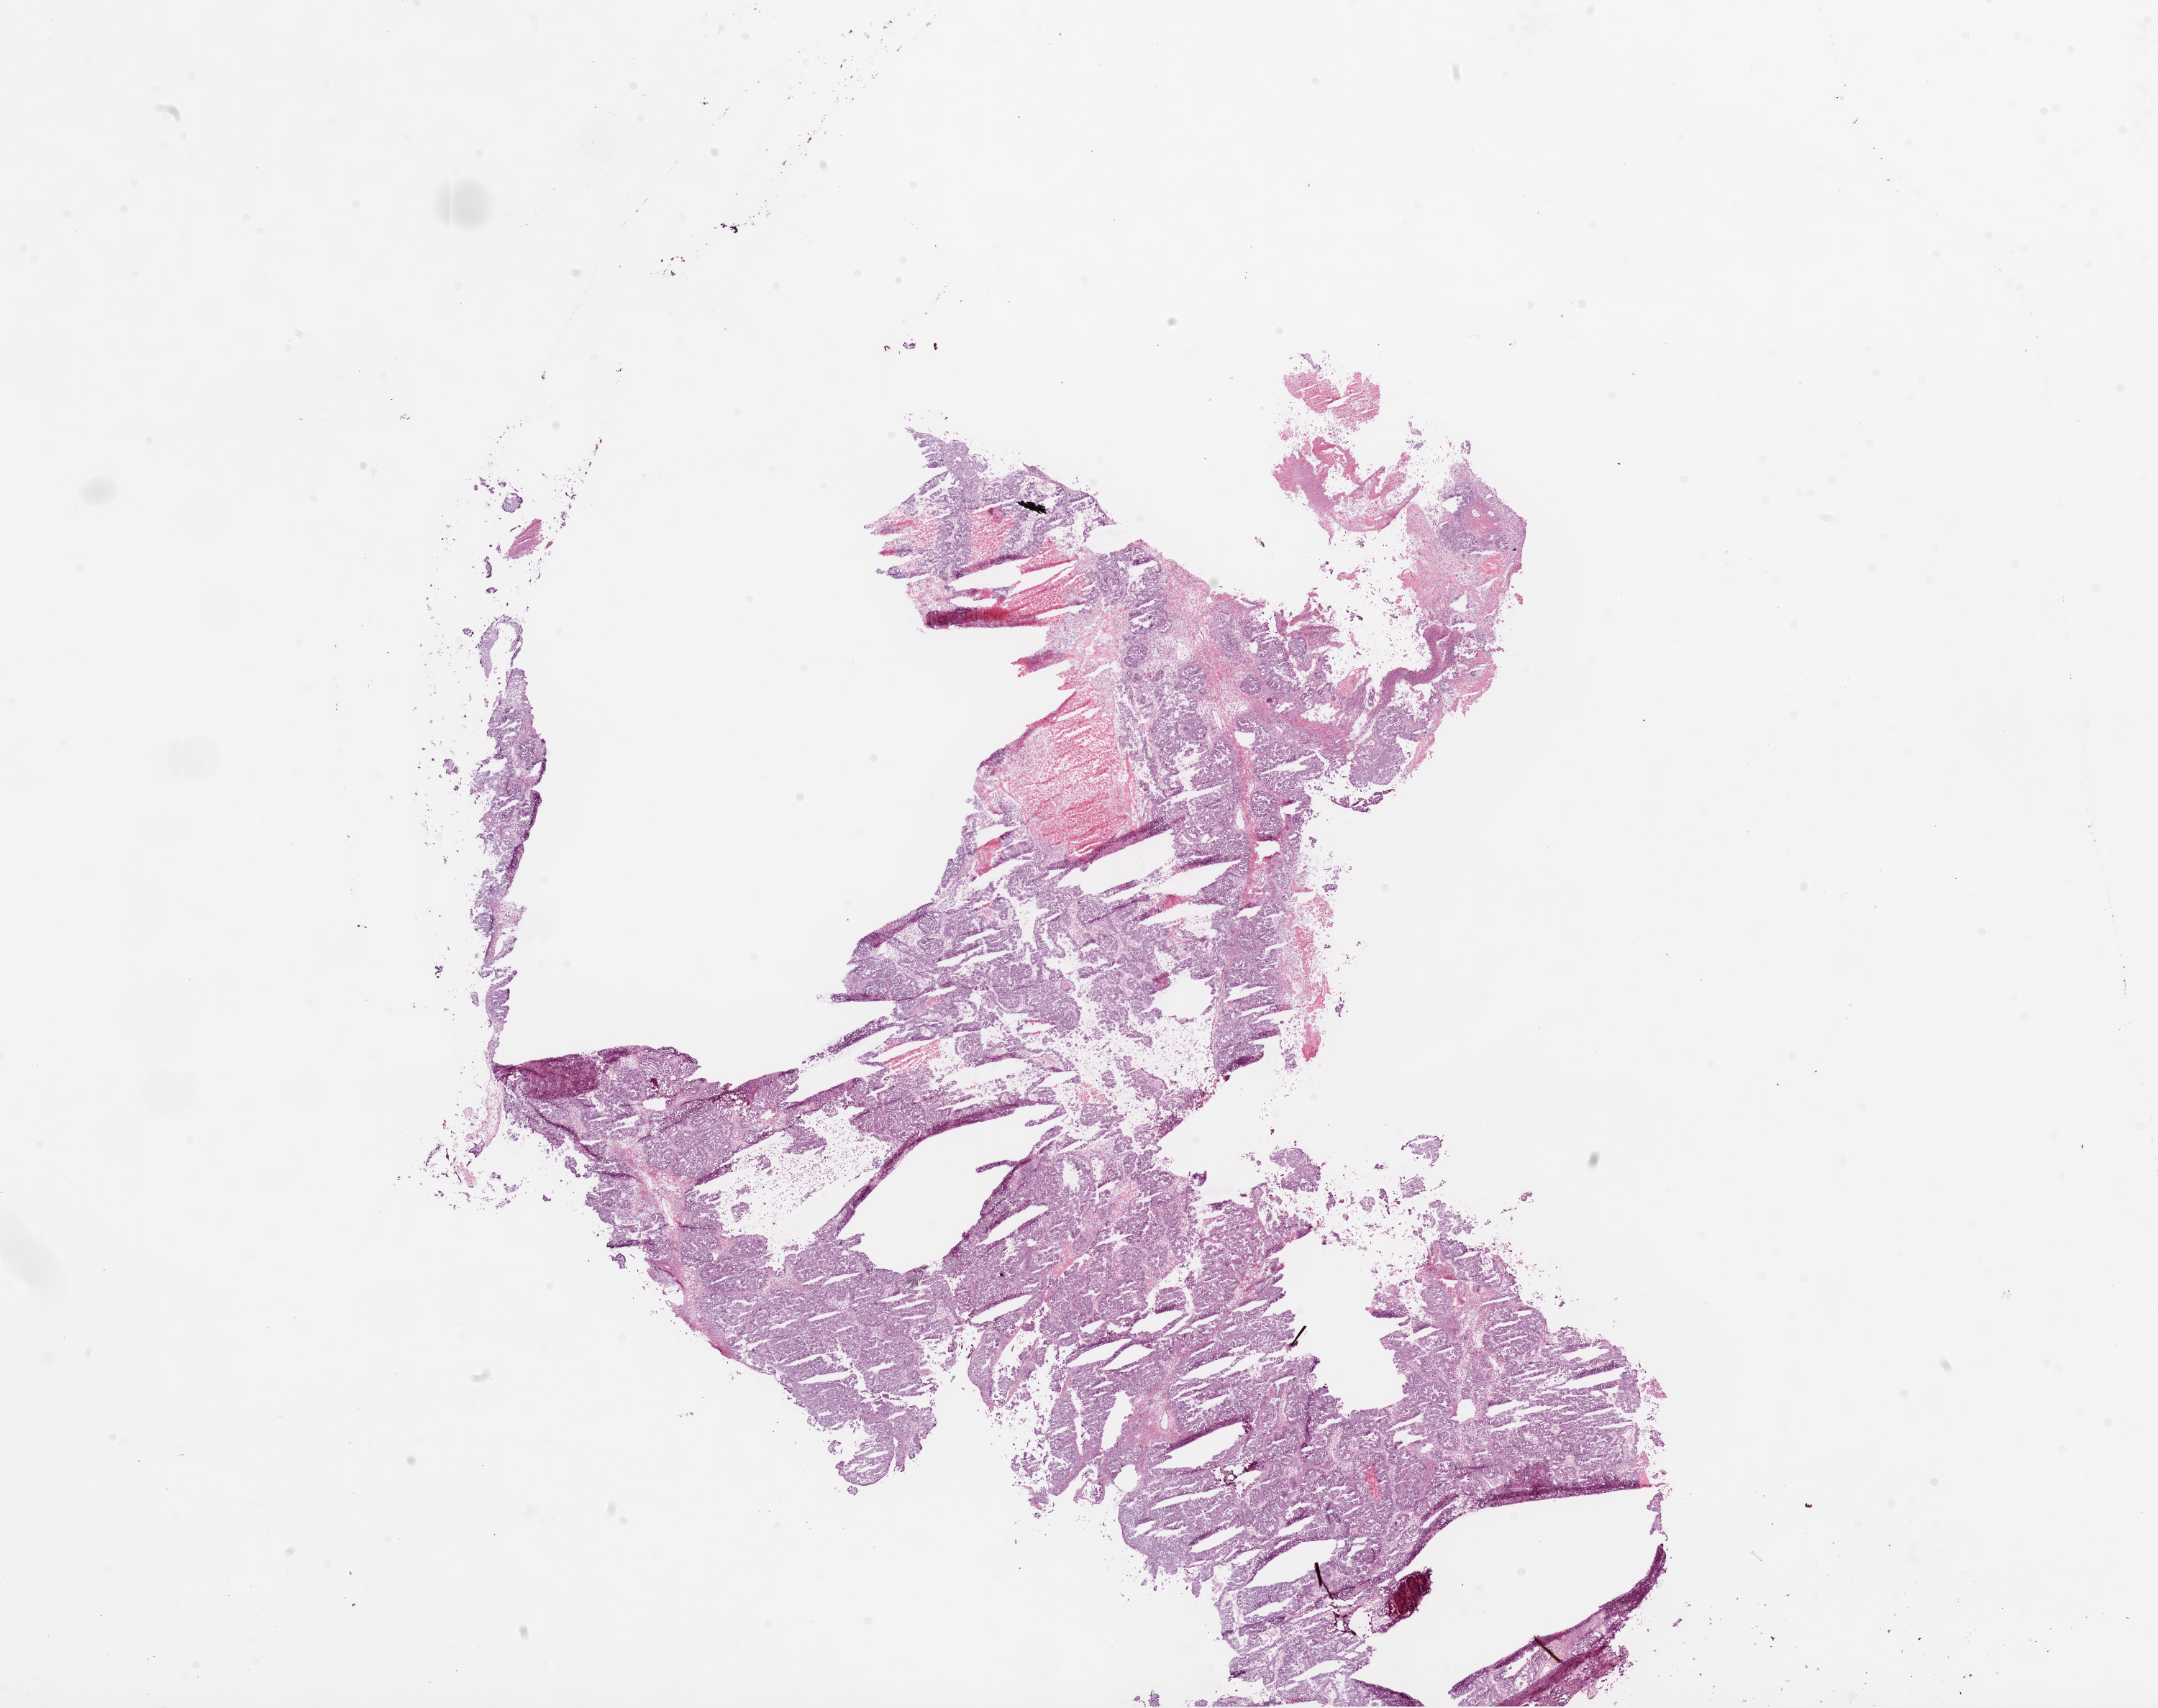
Digitized H&E-stained tissue section (whole slide) — a low-resolution overview of the entire scanned area, about 24.1 x 19.1 mm, frozen section, sample: primary tumour, ovary. Patient: female, age at initial diagnosis 48 years. Histologic grade: G3 (poorly differentiated). Composition of this section per pathologist review: tumour cells 74%, tumour nuclei 90%, normal cells 1%, stromal cells 10%, necrosis 15%.
Histologic diagnosis: Serous cystadenocarcinoma, NOS. FIGO stage: IC. Laterality: left.